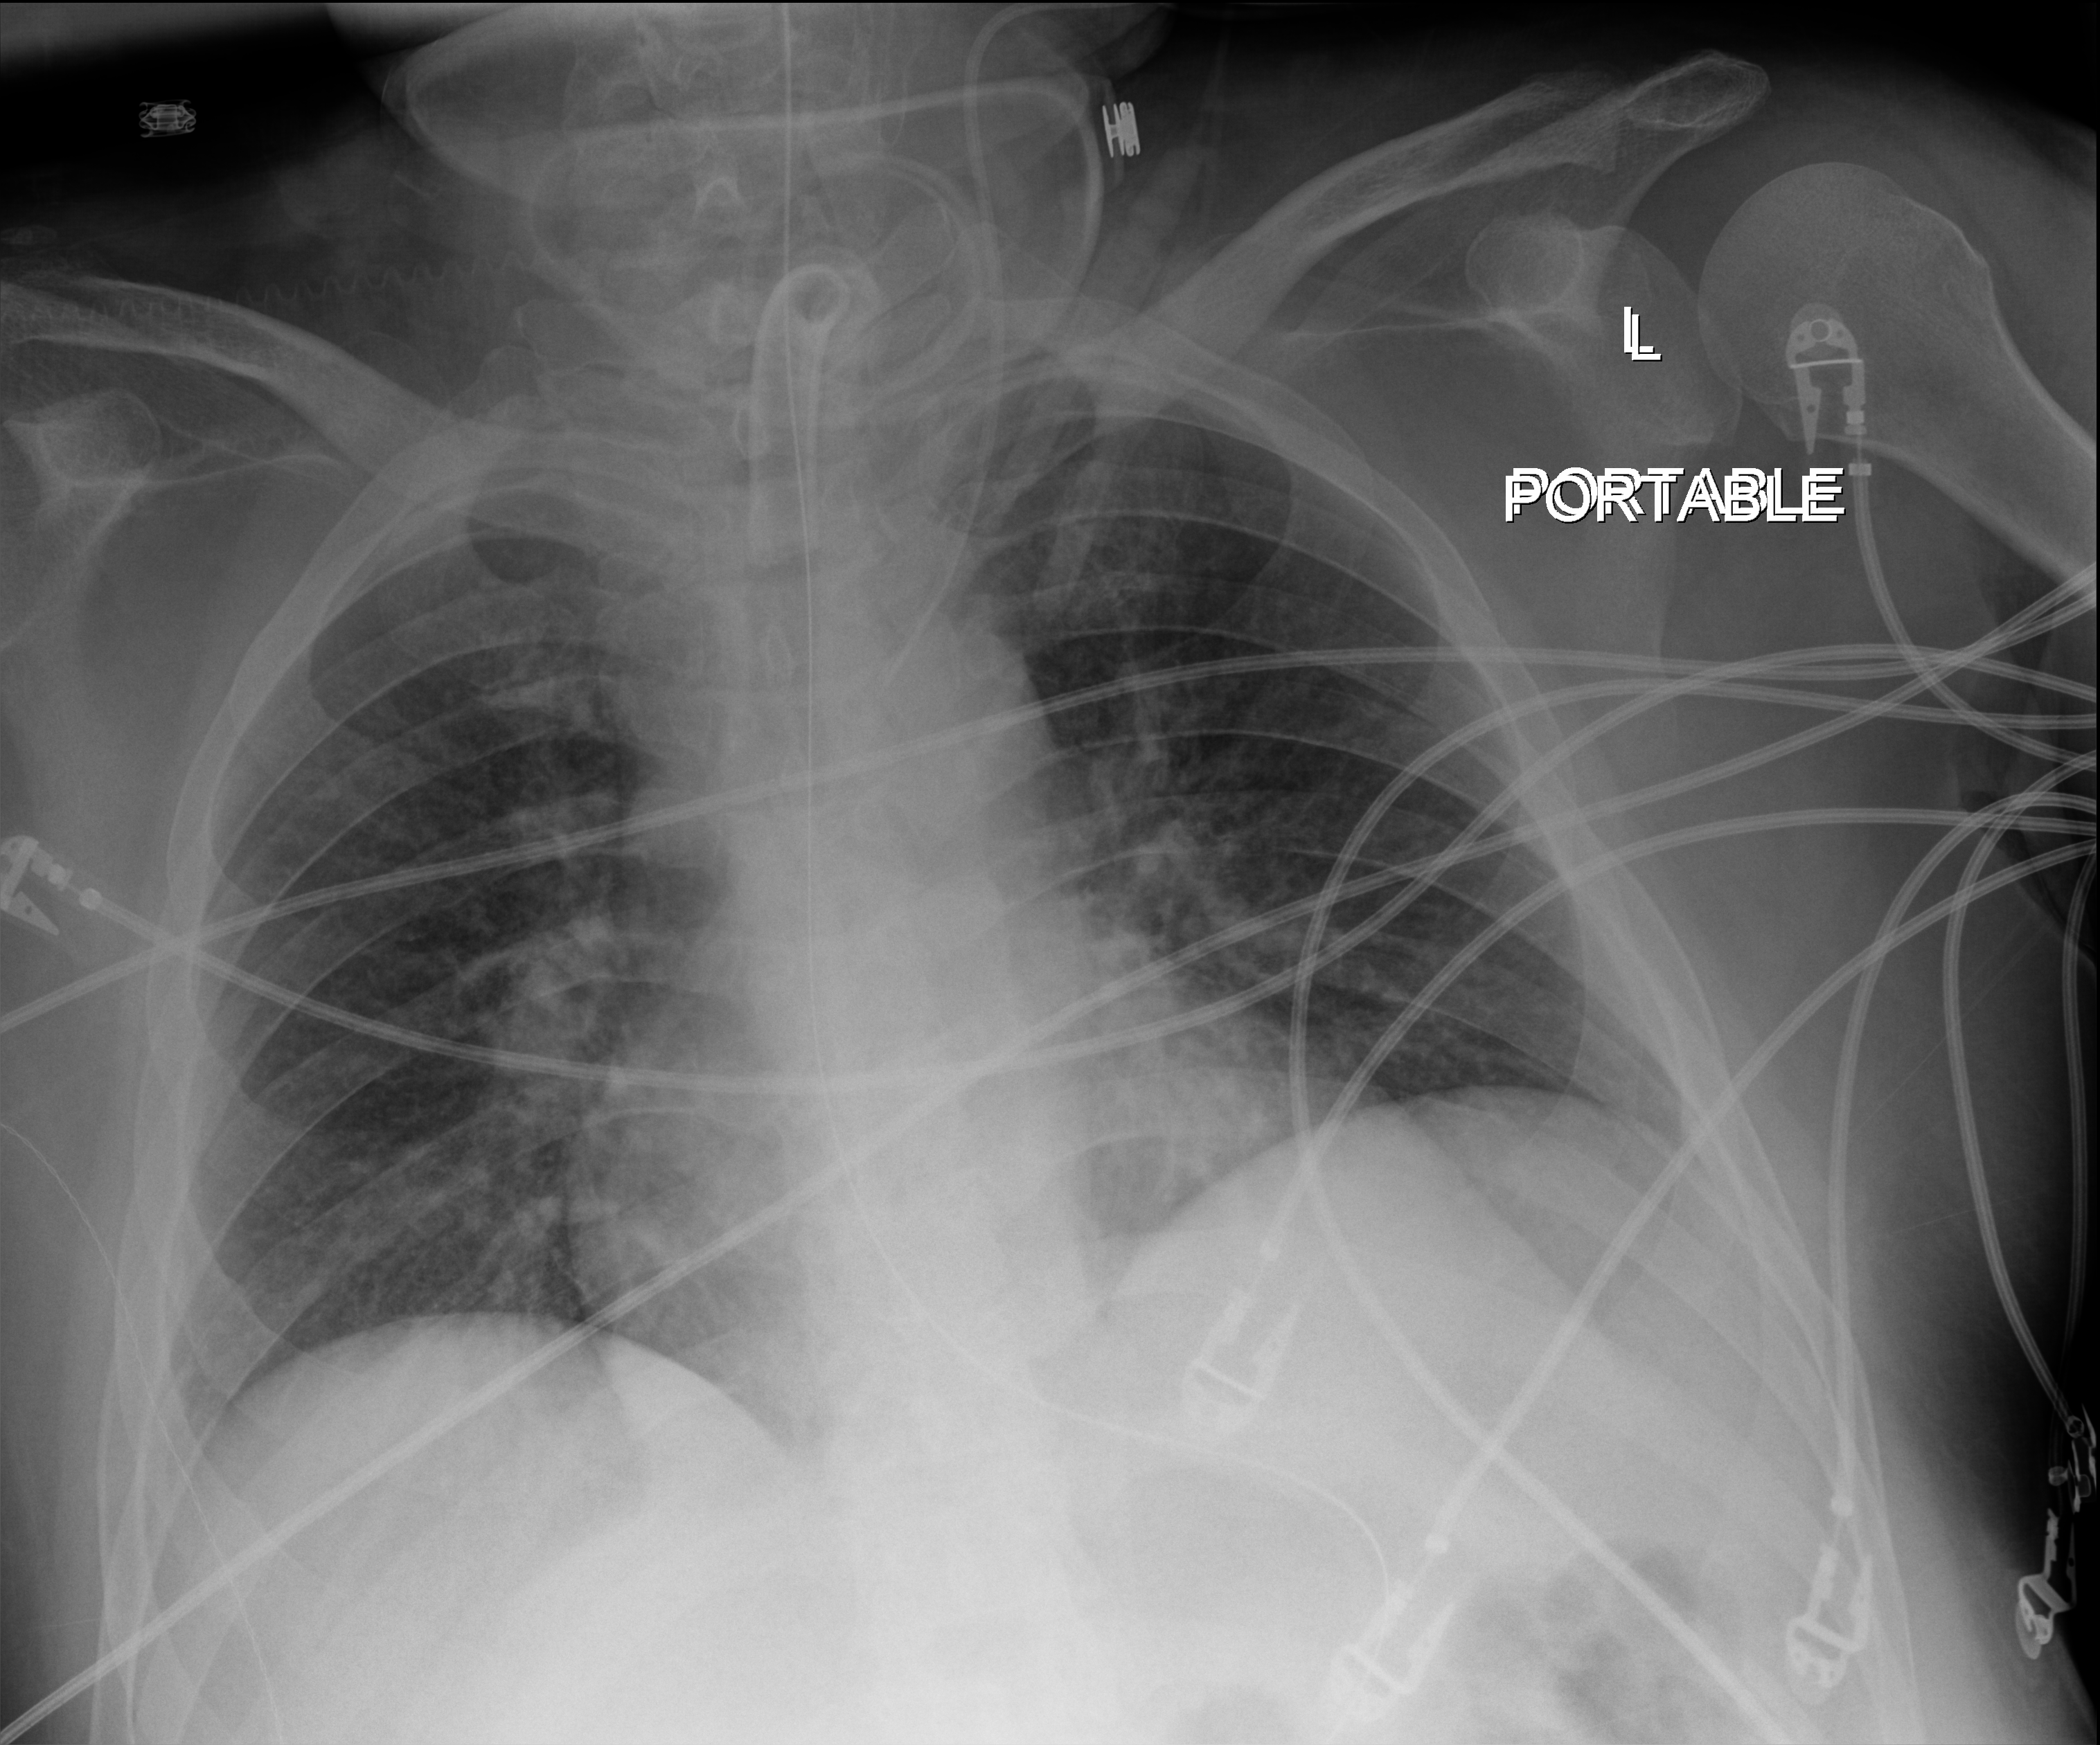
Portable chest radiograph, anteroposterior (AP) projection. Male patient hospitalised with COVID-19, age 18–59 years.
Hospital-stay facts (about this admission, not read from this image; timing relative to this image not recorded): mechanically ventilated during this hospital stay: yes; length of hospital stay: 65 days; admitted to intensive care during this hospital stay: yes.